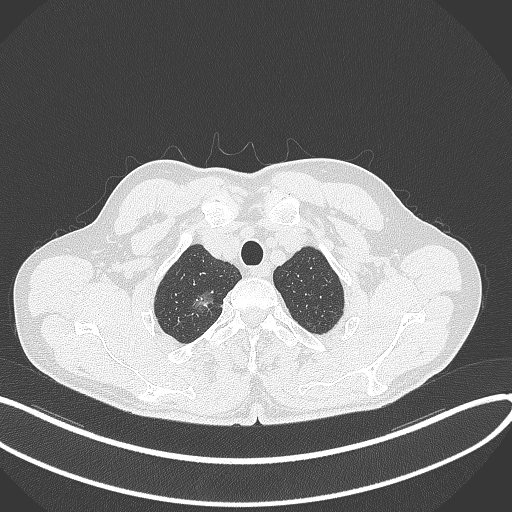
Chest CT, one axial slice. Reconstruction kernel B70f. 120 kVp. Lung window (W 1500 / L -600 HU). 1 mm slice thickness. 512 × 512 image matrix, field of view 400 × 400 mm. Patient: male, 58 years. Case-level facts recorded for this patient, not image findings: clinical TNM (as recorded): T1c N0 M0; histopathological grade: G1-2.
Outlined on this slice (bounding box drawn by a radiologist):
- lung tumour (recorded histology: adenocarcinoma): bounding box [x1, y1, x2, y2] px = [188, 284, 218, 313]